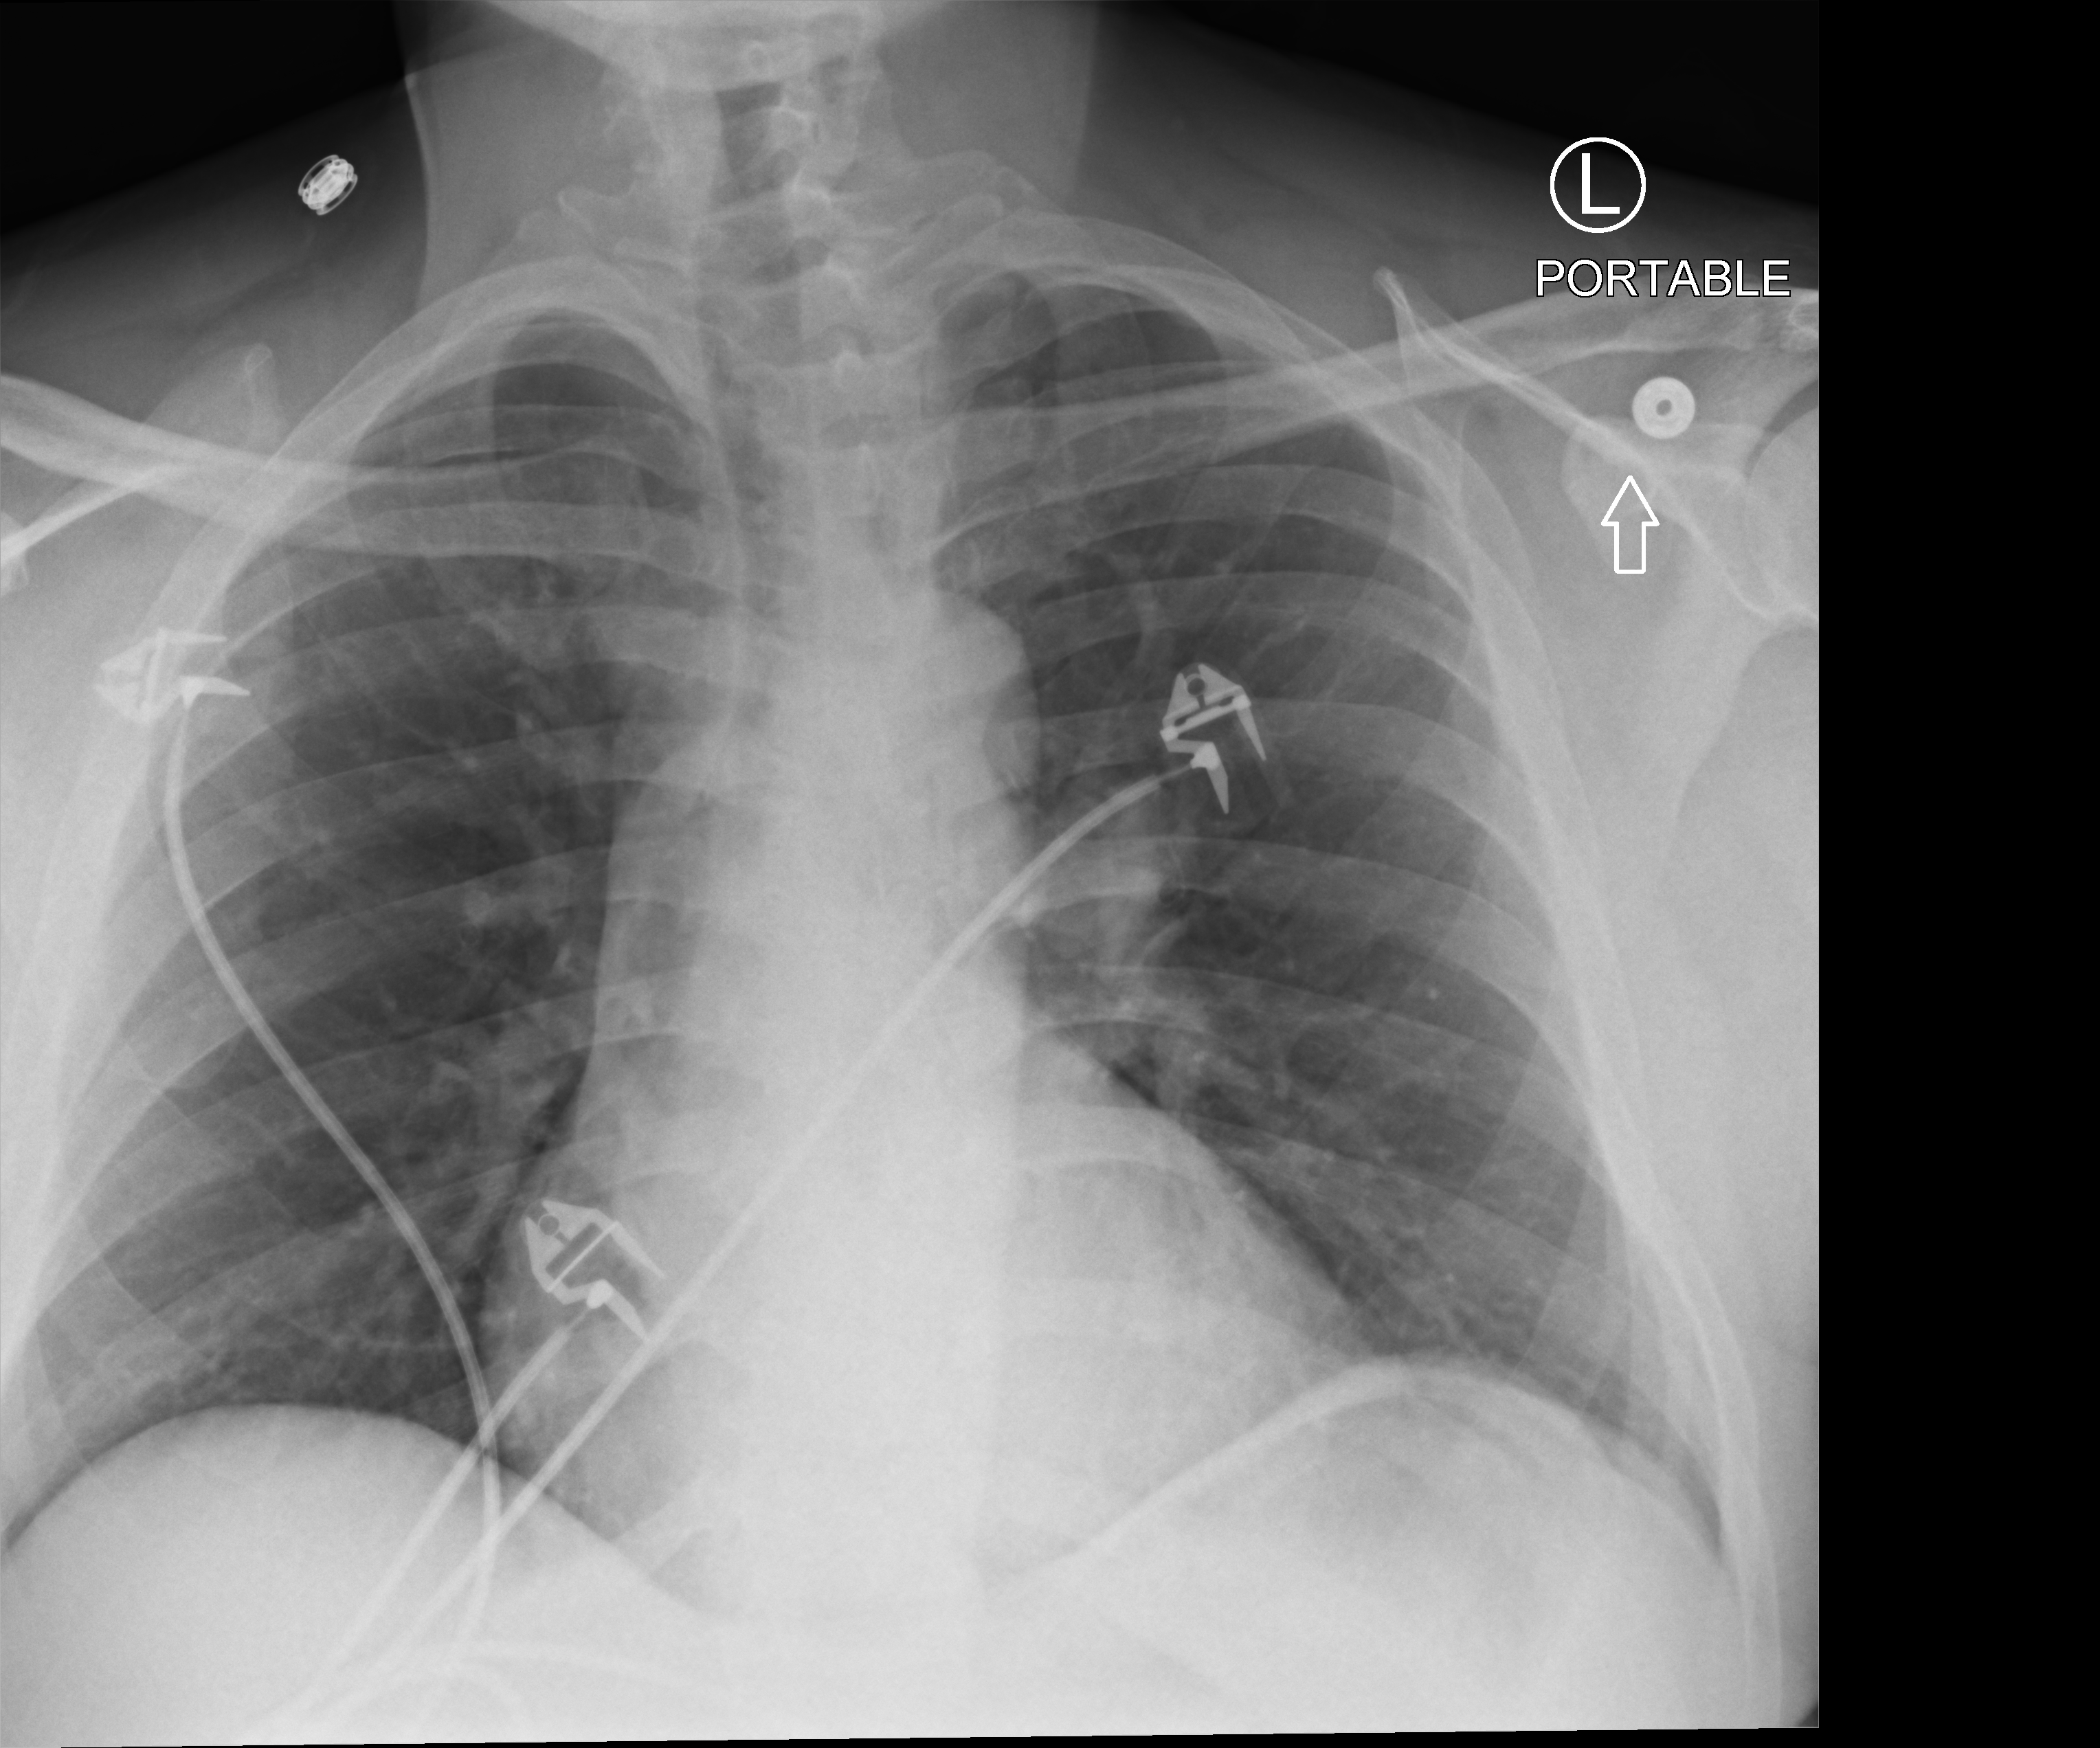
Chest X-ray (portable), anteroposterior (AP) projection. Male patient hospitalised with COVID-19, age 18–59 years.
From the hospital-stay record, not from the radiograph (when in the stay this image was taken is not recorded): length of hospital stay: 36 days; diabetes (admission record): yes; mechanically ventilated during this hospital stay: no.